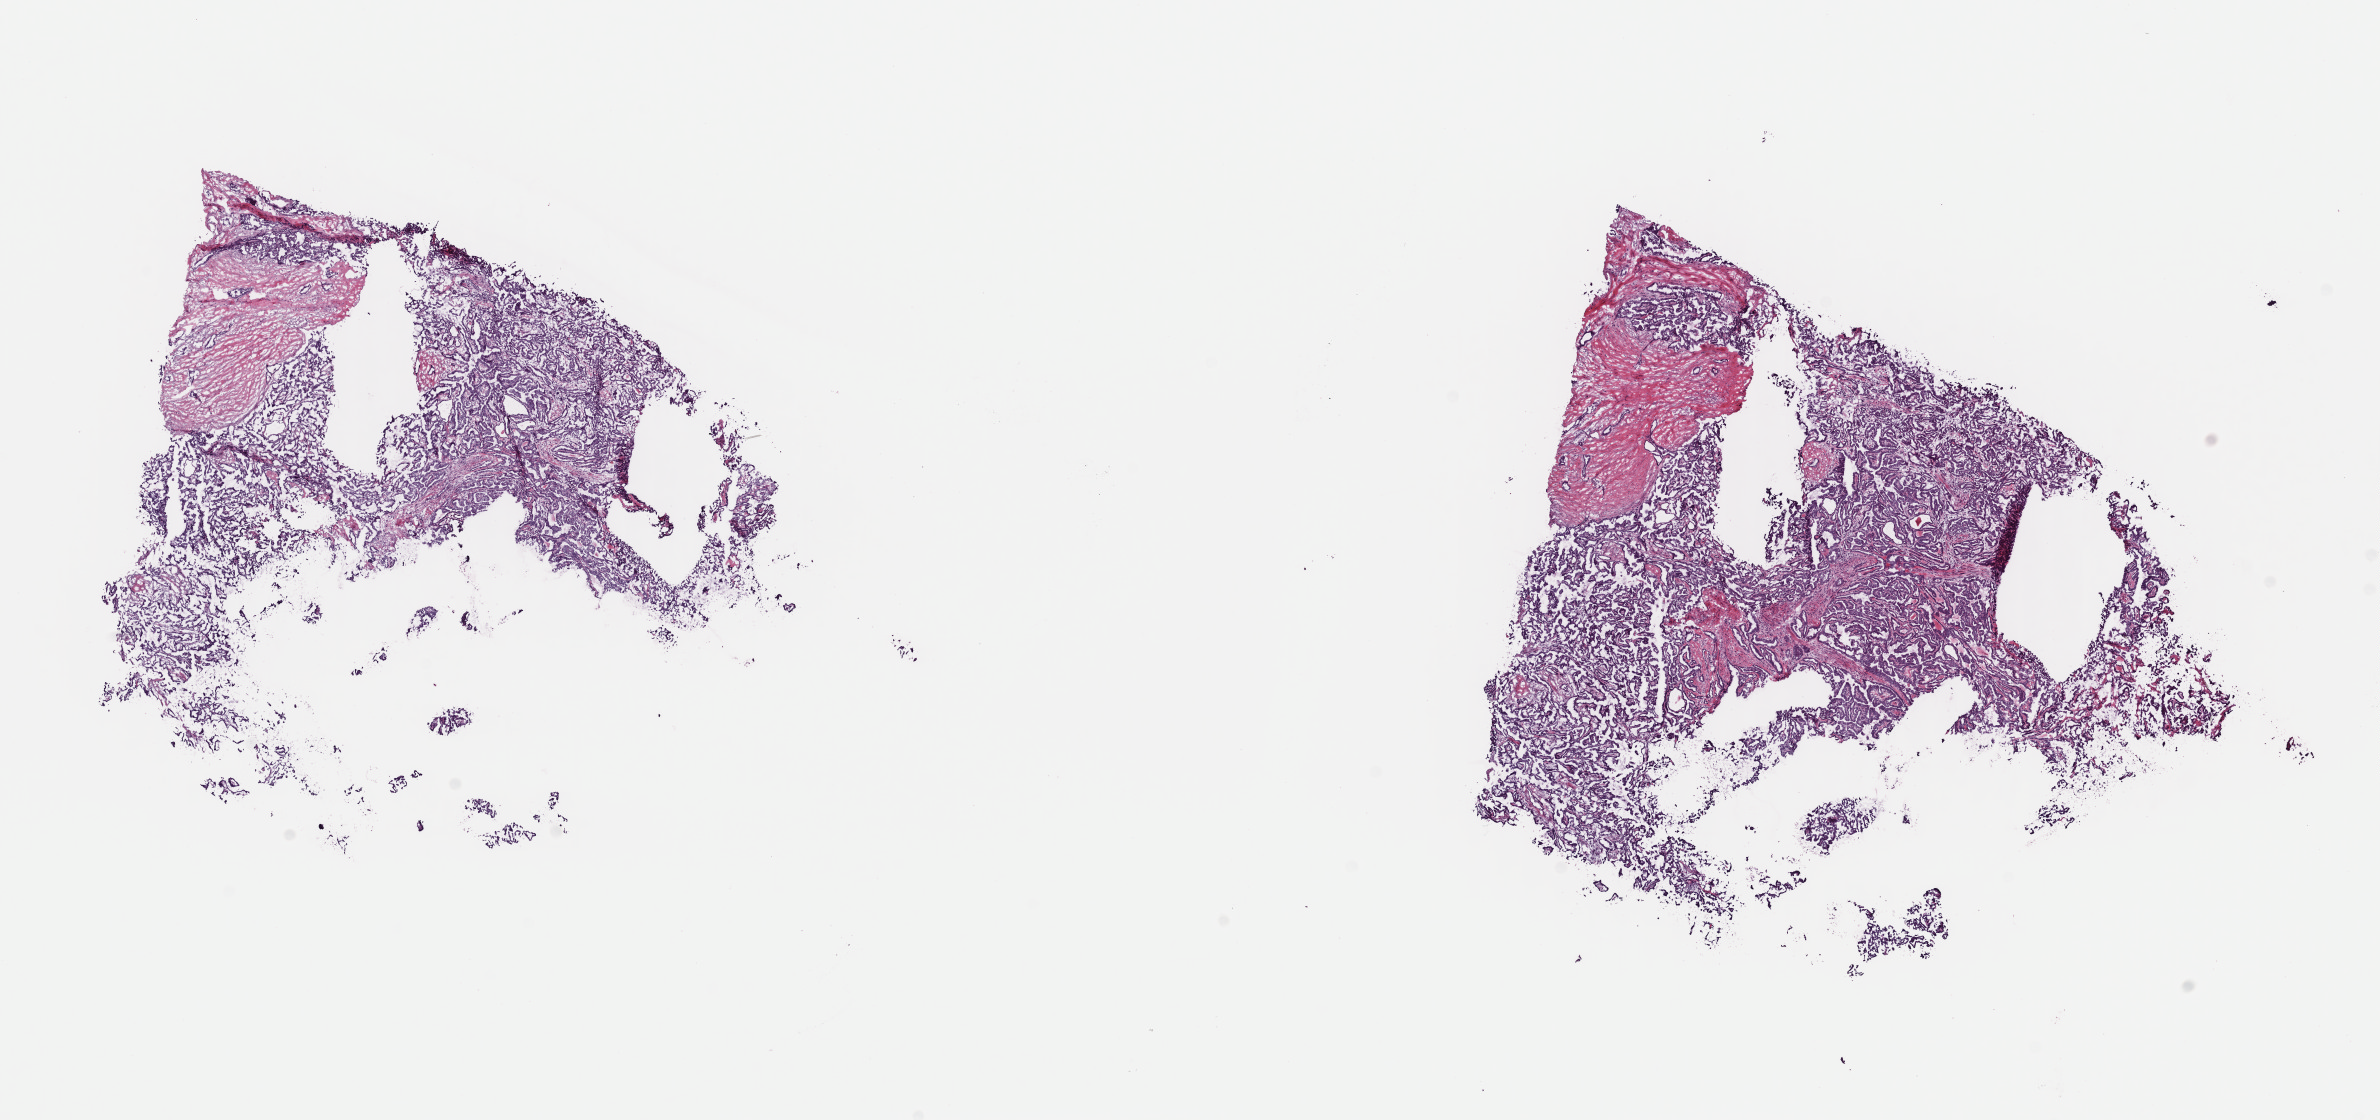
Whole-slide histology image, H&E-stained, a low-resolution overview of the entire scanned area, about 18.8 x 8.8 mm (from a 40x scan), frozen section from the top of the tissue portion, thyroid, primary tumour sample. Patient: female, age at initial diagnosis 57 years. Slide review estimates, as recorded: tumour cells 95%, tumour nuclei 80%, normal cells 0%, stromal cells 5%, necrosis 0%. Inflammatory infiltration, as recorded: lymphocyte infiltration 0%, monocyte infiltration 0%, neutrophil infiltration 0%.
Laterality: bilateral. Diagnosis: Papillary carcinoma, columnar cell (thyroid gland). AJCC pathologic stage: III (7th edition).